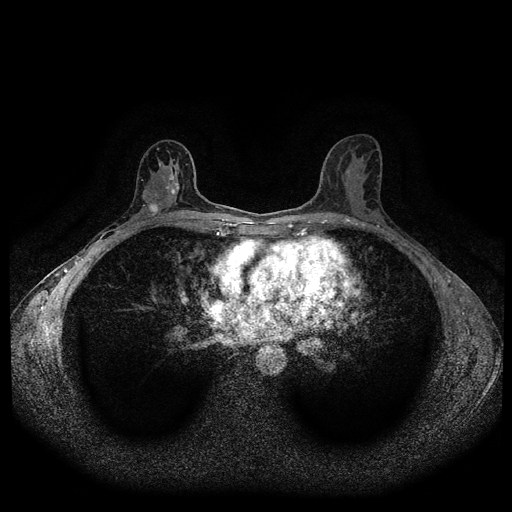
Breast MRI (dynamic contrast-enhanced, multi-phase), one axial slice. Slice 57 of 116 in the series (ordered by position). Dynamic contrast-enhanced series, time point 2 of 5 at this slice position (early post-contrast). 1.5 T. TE 2.6 ms, TR 5.3 ms. 512 × 512 image matrix, field of view 350 × 350 mm. Patient: female, 50 years.
Annotated regions visible in this slice (semi-automatic segmentation, software-assisted and operator-edited):
- breast lesion (labelled 'tumour' in the annotation; benign lesions carry a separate 'benign' label): box from (x=149, y=203) to (x=159, y=216) px